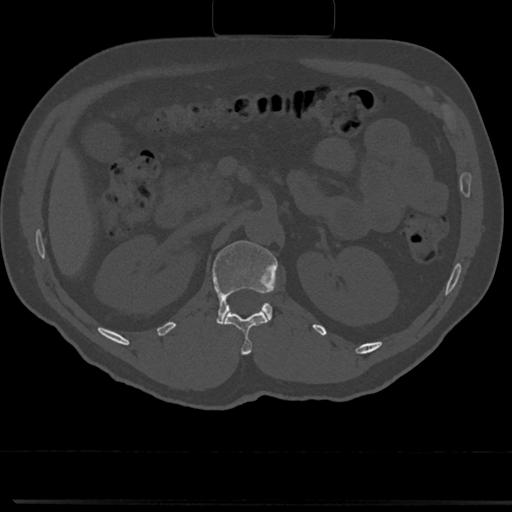
CT including the spine, one axial slice; slice 108 of 817 in the series (ordered by position); bone window (W 1800 / L 400 HU); 0.5 mm slice thickness; 512 × 512 image matrix. Male patient, age 61 years. From the clinical record (not read from this slice): primary cancer: prostate.
Annotated regions visible in this slice (semi-automatic segmentation, software-assisted and operator-edited):
- L1 vertebra: bounding box [x1, y1, x2, y2] px = [194, 240, 278, 326]
- T12 vertebra: [224, 311, 268, 353]